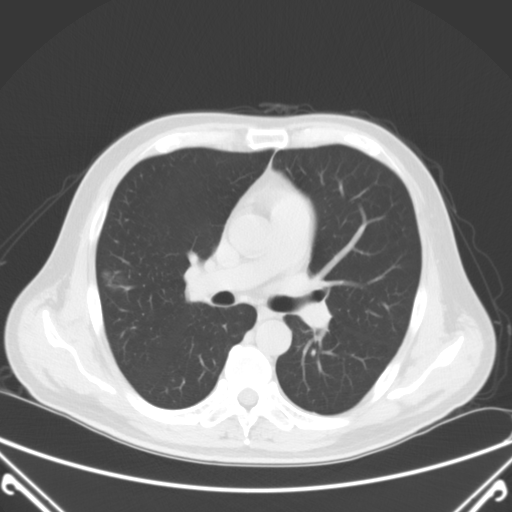
Chest CT, one axial slice. Position 44 of 72 along the scan axis. Lung window (W 1500 / L -600 HU). 5 mm slice thickness. 512 × 512 image matrix, field of view 380 × 380 mm. Male patient, age 64 years. From the clinical record (not read from this slice): clinical TNM (as recorded): T1c N0 M0; histopathological grade: G2.
Structures marked on this image (bounding box drawn by a radiologist):
- lung tumour (recorded histology: adenocarcinoma): box from (x=92, y=263) to (x=130, y=304) px